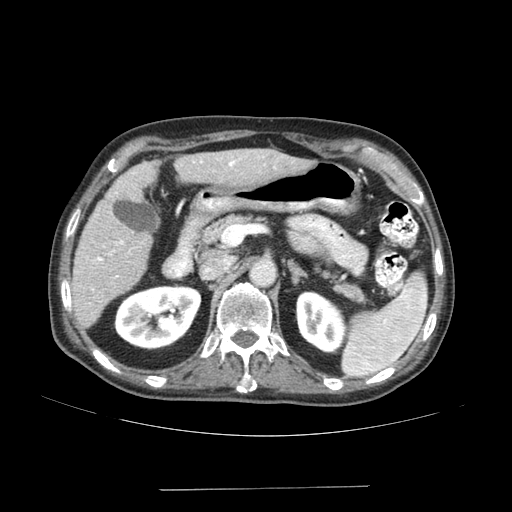
Contrast-enhanced abdominal CT (liver protocol), one axial slice. Position 82 of 192 along the scan axis. 120 kVp. Soft-tissue window (W 400 / L 40 HU). 2.5 mm slice thickness. 512 × 512 image matrix, field of view 400 × 400 mm. Case-level facts recorded for this patient, not image findings: diagnosis: hepatocellular carcinoma (patient treated with transarterial chemoembolisation; whether this scan precedes or follows treatment is not stated here); TNM stage (as recorded): Stage-IVA; Child-Pugh class: A; tumour differentiation: poorly differentiated.
Structures marked on this image (semi-automatic segmentation, software-assisted and operator-edited):
- liver parenchyma outside the tumour (the mass and vessels are separate outlines, so this box may not span the whole liver): bounding box <70,150,312,327> (left, top, right, bottom; pixels)
- liver vessels: <97,160,236,261>